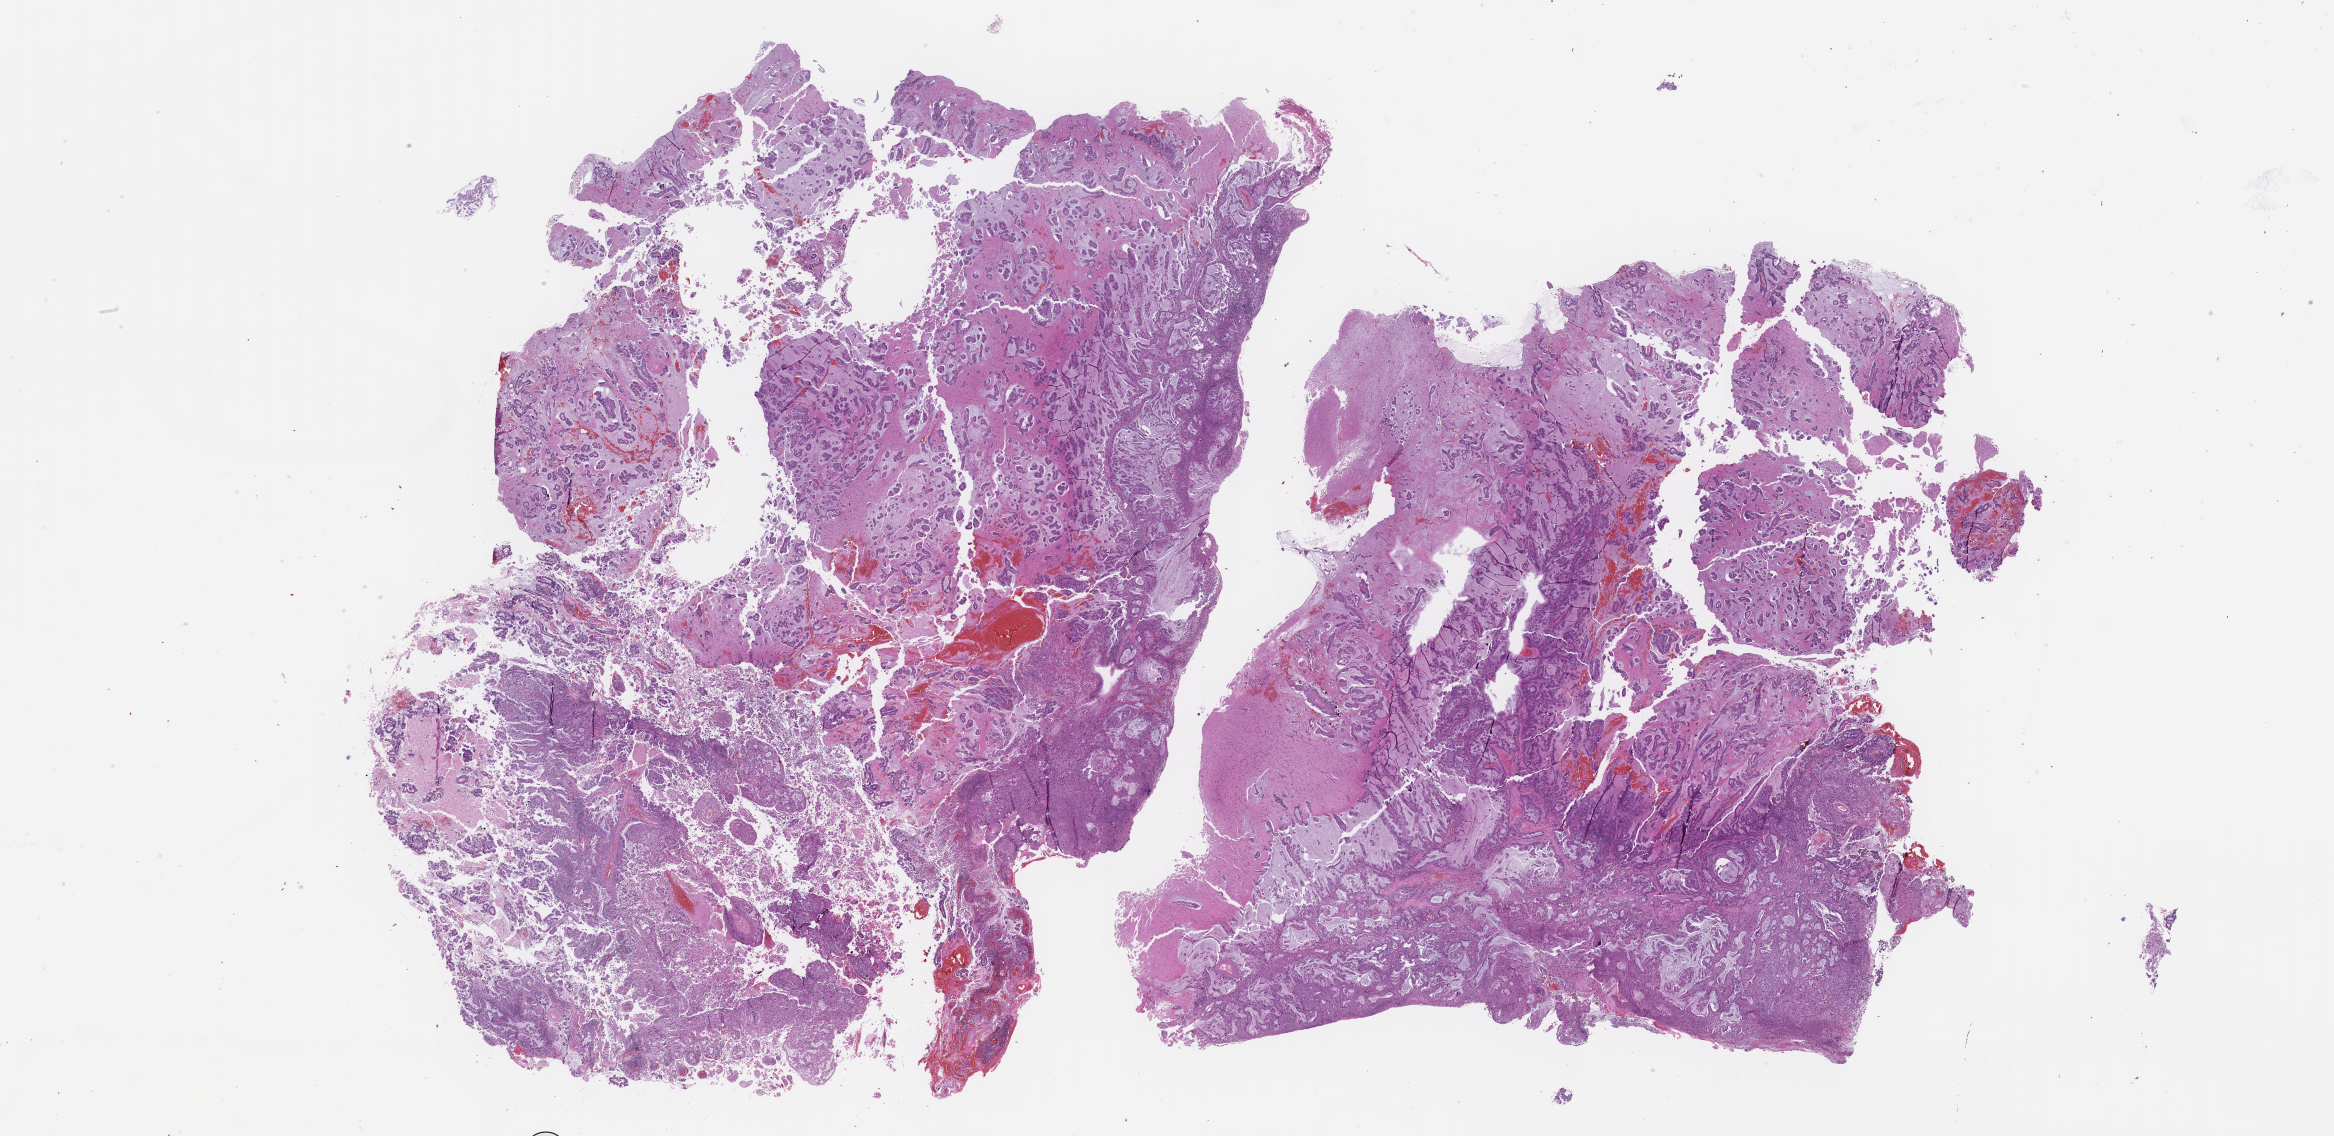
Haematoxylin and eosin whole-slide image — a low-resolution overview of the entire scanned area, about 37.7 x 18.3 mm, formalin-fixed, paraffin-embedded (FFPE) tissue. Patient: female.
This section: metastatic tumor tissue. Patient diagnosis (primary): Non-Small Cell Lung Carcinoma.